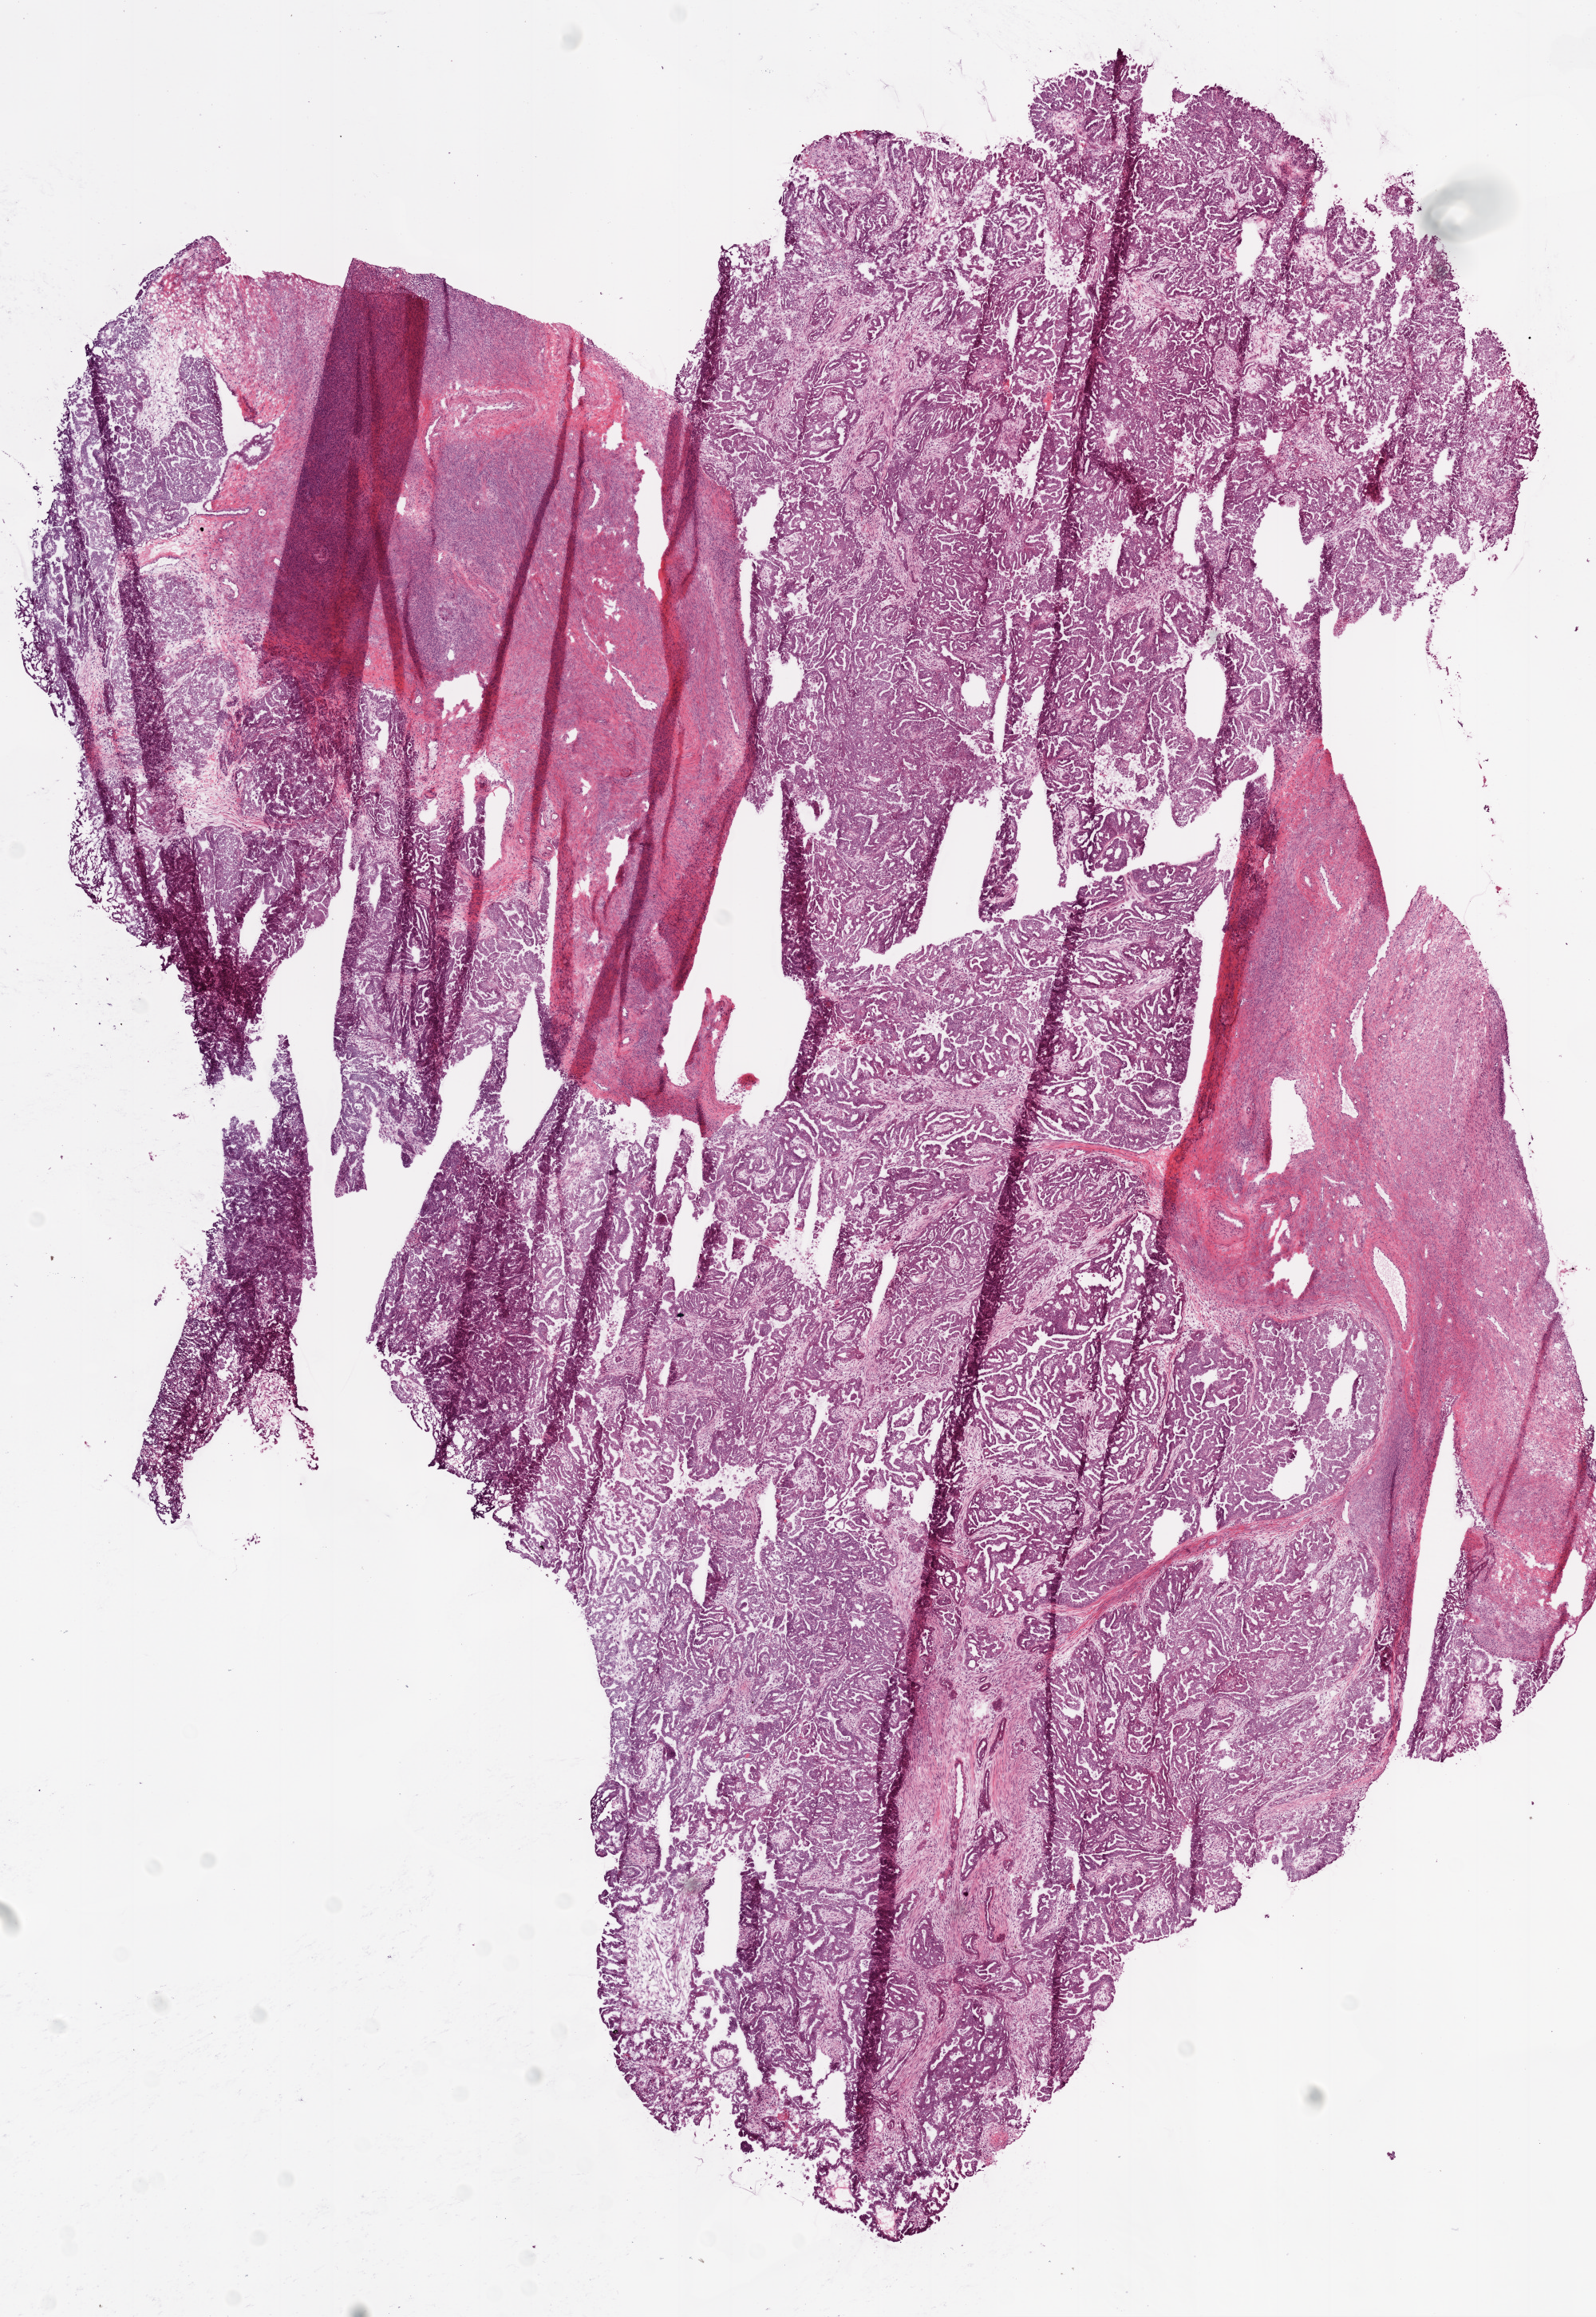
Digitized H&E-stained tissue section (whole slide), a low-resolution overview of the entire scanned area, about 8.0 x 11.6 mm (slide scanned at 20x). Frozen section. Ovary, primary tumour sample. Female patient; age at initial diagnosis 45 years. Histologic grade: GX (grade cannot be assessed). Composition of this section per pathologist review: tumour cells 80%, tumour nuclei 80%, normal cells 0%, stromal cells 20%, necrosis 0%.
- laterality: bilateral
- FIGO stage: IIIC
- histologic diagnosis: Serous cystadenocarcinoma, NOS